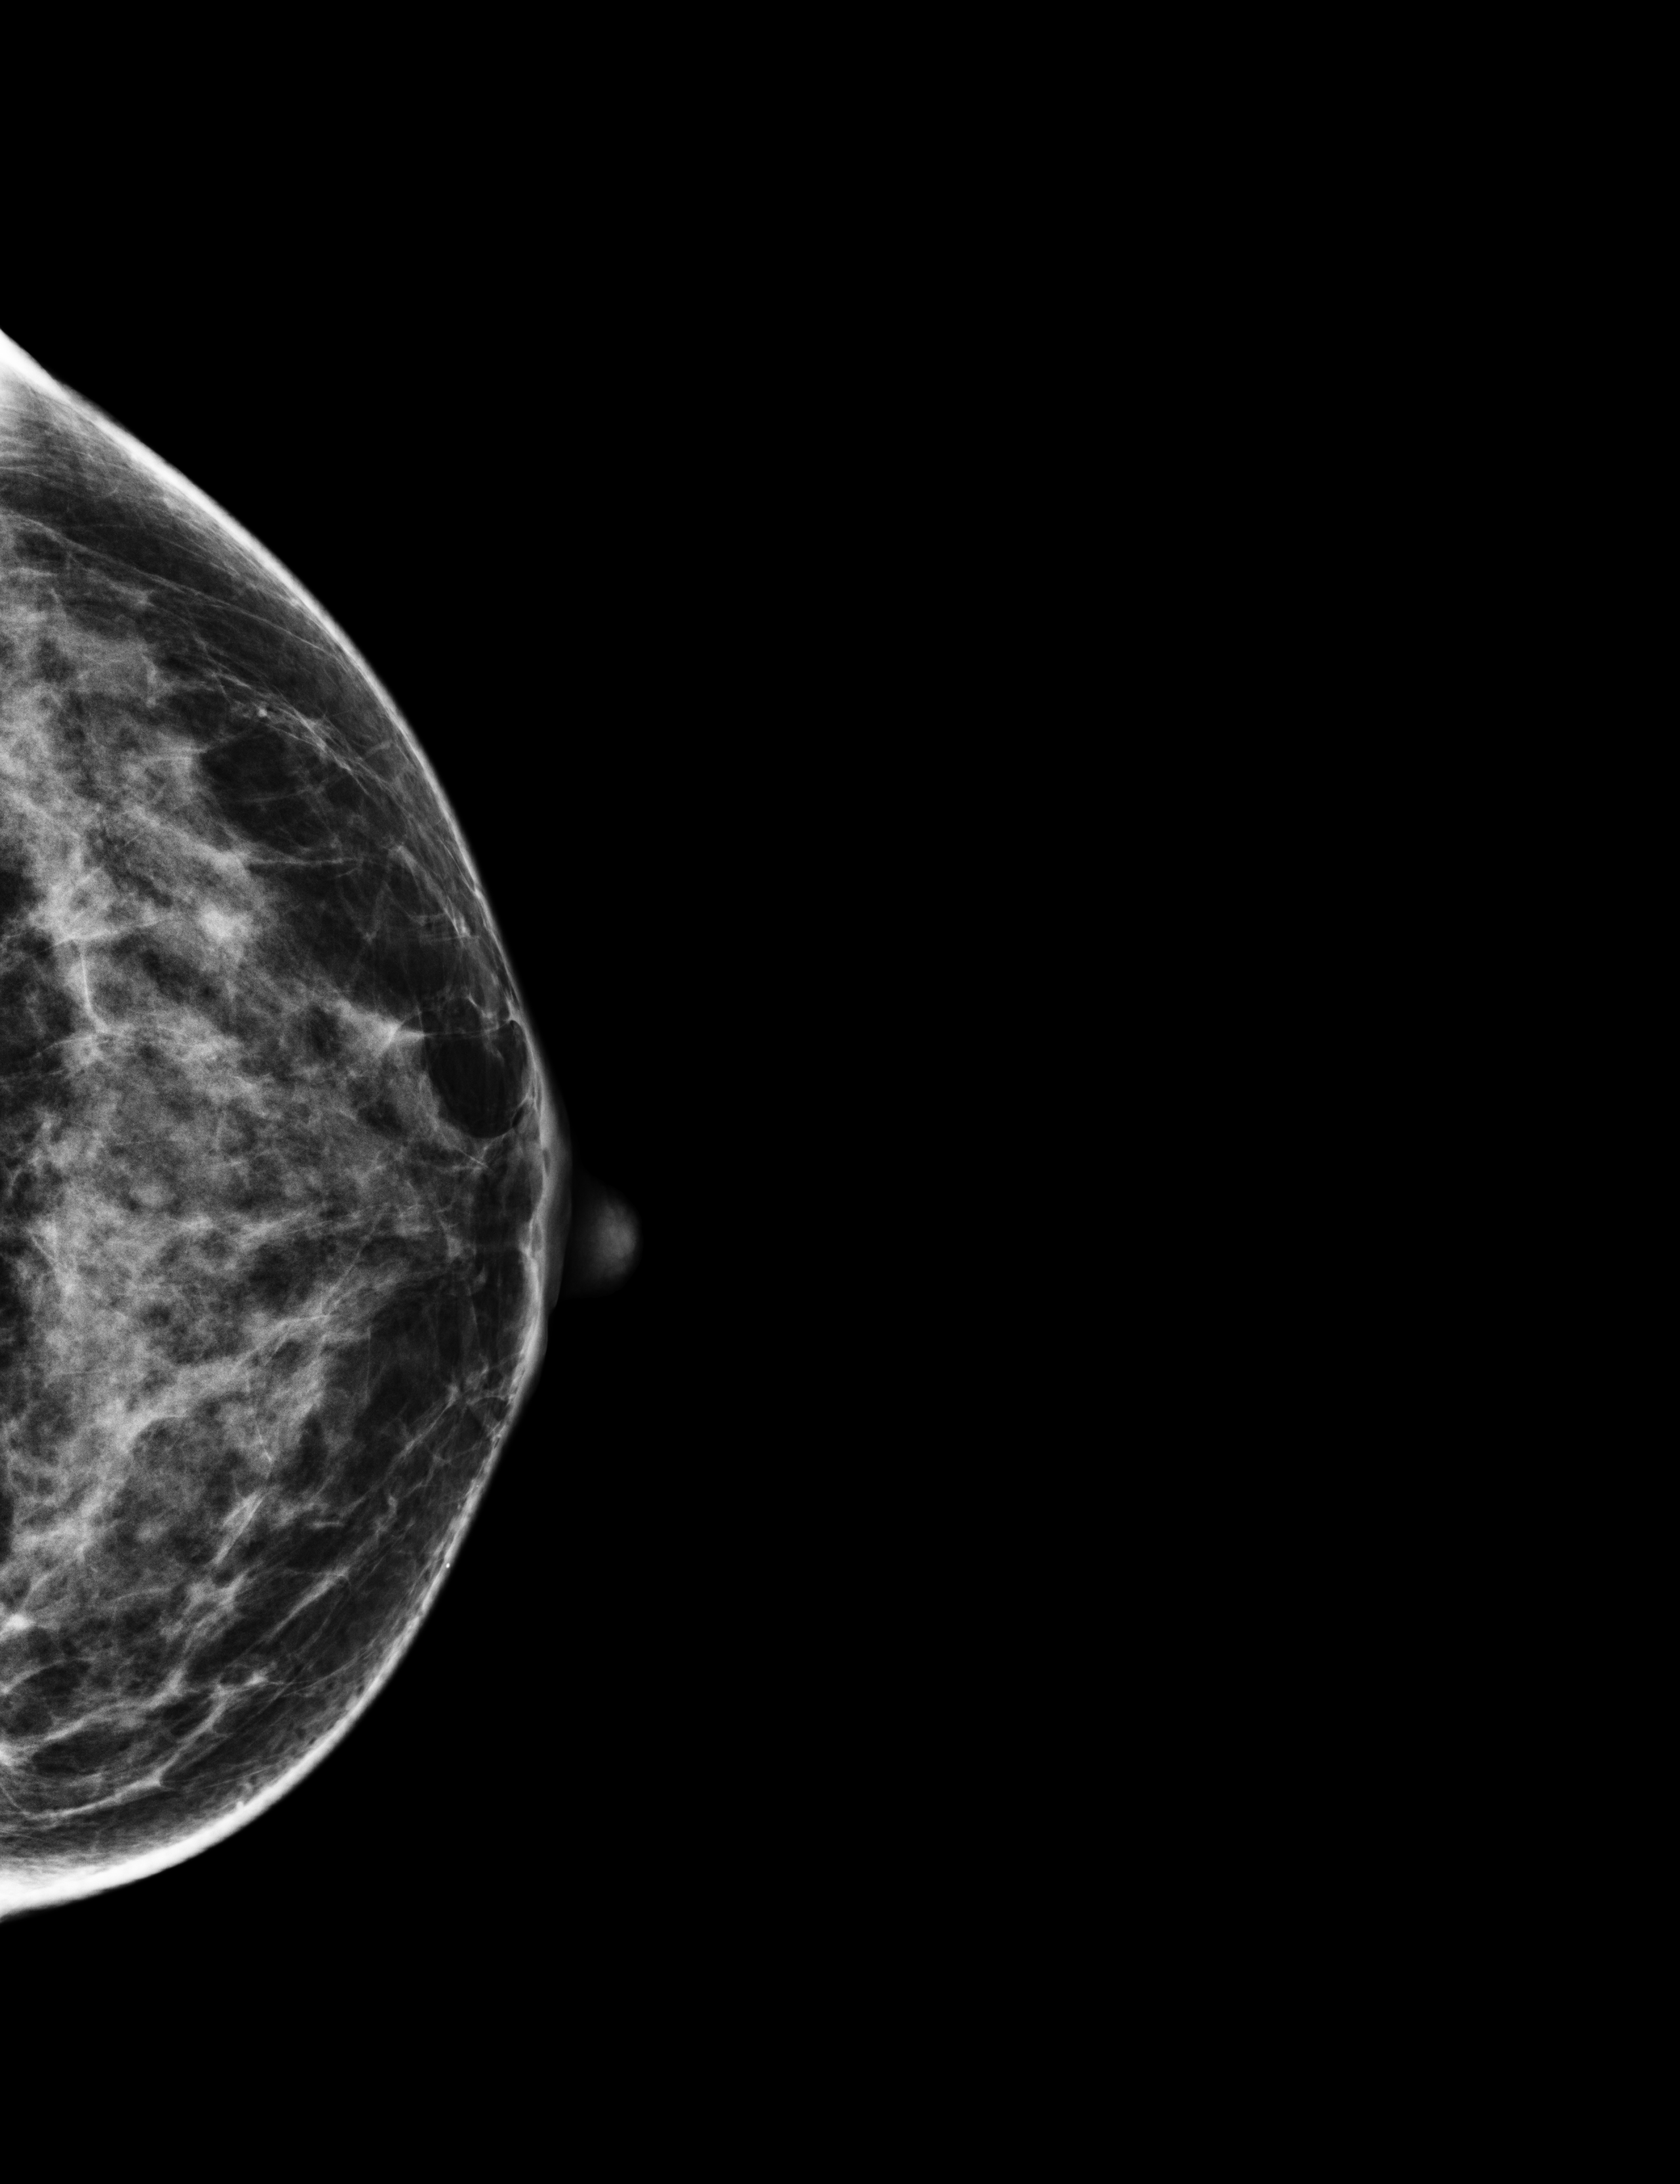
Digital mammogram (FFDM), left breast, craniocaudal (CC) view, screening examination, compressed breast thickness 58 mm, system: Selenia Dimensions. Patient: female, 54 years.
BI-RADS breast density category at the screening exam (both breasts, scale 1–4): 3. Final BI-RADS category for the screening round (tomosynthesis exam, both breasts): category 1. Recall: no recall after this screen.